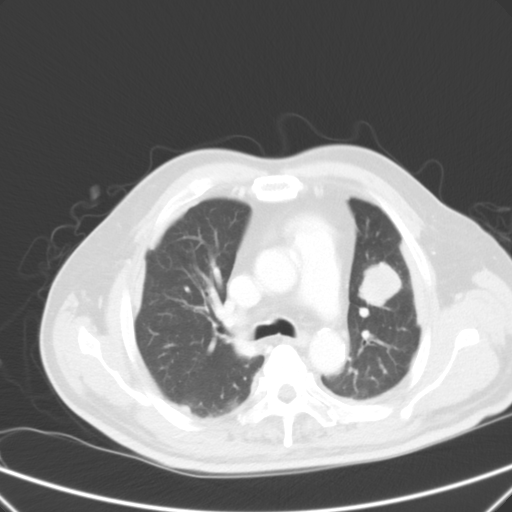
Chest CT, one axial slice; slice 40 of 59 in the series (ordered by position); intravenous contrast given; lung window (W 1500 / L -600 HU); 5 mm slice thickness; 512 × 512 image matrix. Male patient, age 66 years. From the clinical record (not read from this slice): clinical TNM (as recorded): T1c N3 M1a.
Outlined on this slice (bounding box drawn by a radiologist):
- lung tumour (recorded histology: squamous cell carcinoma): bounding box (x1, y1, x2, y2) in pixels: (353, 257, 405, 311)